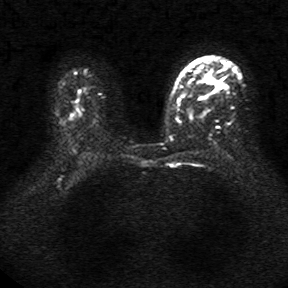
Breast MRI, one axial slice. Diffusion-weighted series; image 2 of 4 stored at this slice position (different b-values; order by instance number). 1.5 T. 5 mm slice thickness. 288 × 288 image matrix, field of view 340 × 340 mm. Female patient.
Annotated regions visible in this slice (expert manual segmentation):
- tumour on diffusion-weighted imaging: bounding box <205,73,214,83> (left, top, right, bottom; pixels)